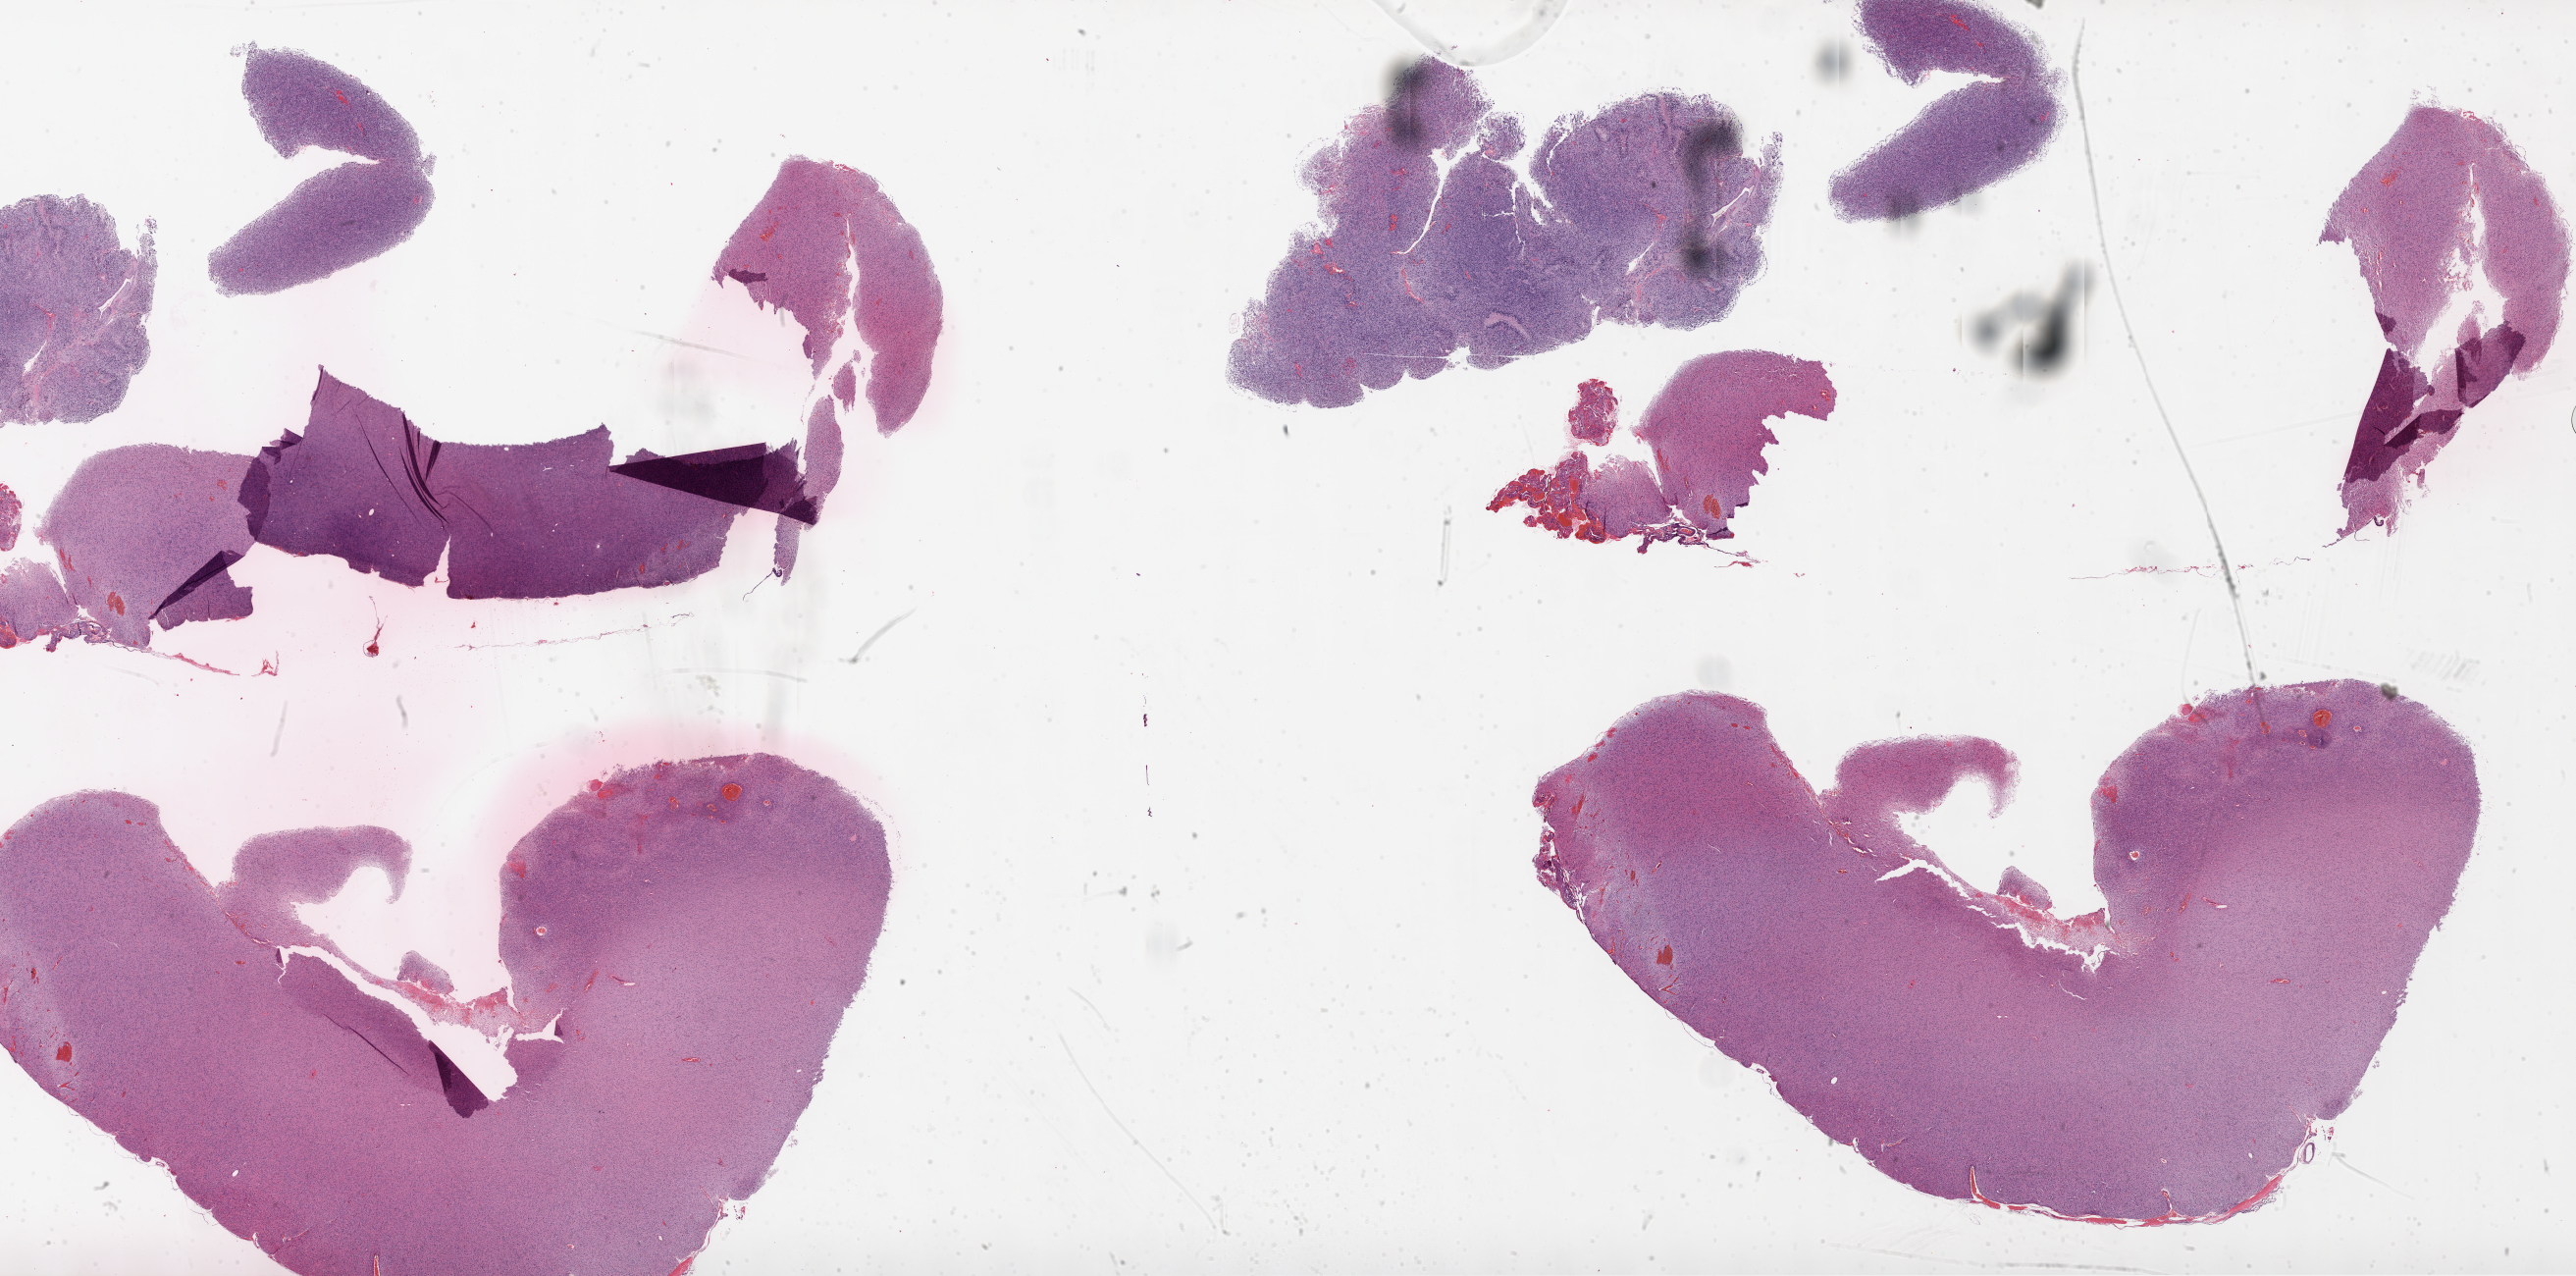
Digitized Hematoxylin and eosin (H&E) stained tissue section (whole slide), shown as a low-resolution overview of the whole scanned area (about 42.1 x 20.9 mm). Formalin-fixed paraffin-embedded (FFPE) diagnostic section. Sample: primary tumour, brain. Patient: female, age at initial diagnosis 63 years.
Pathologic diagnosis: Glioblastoma.